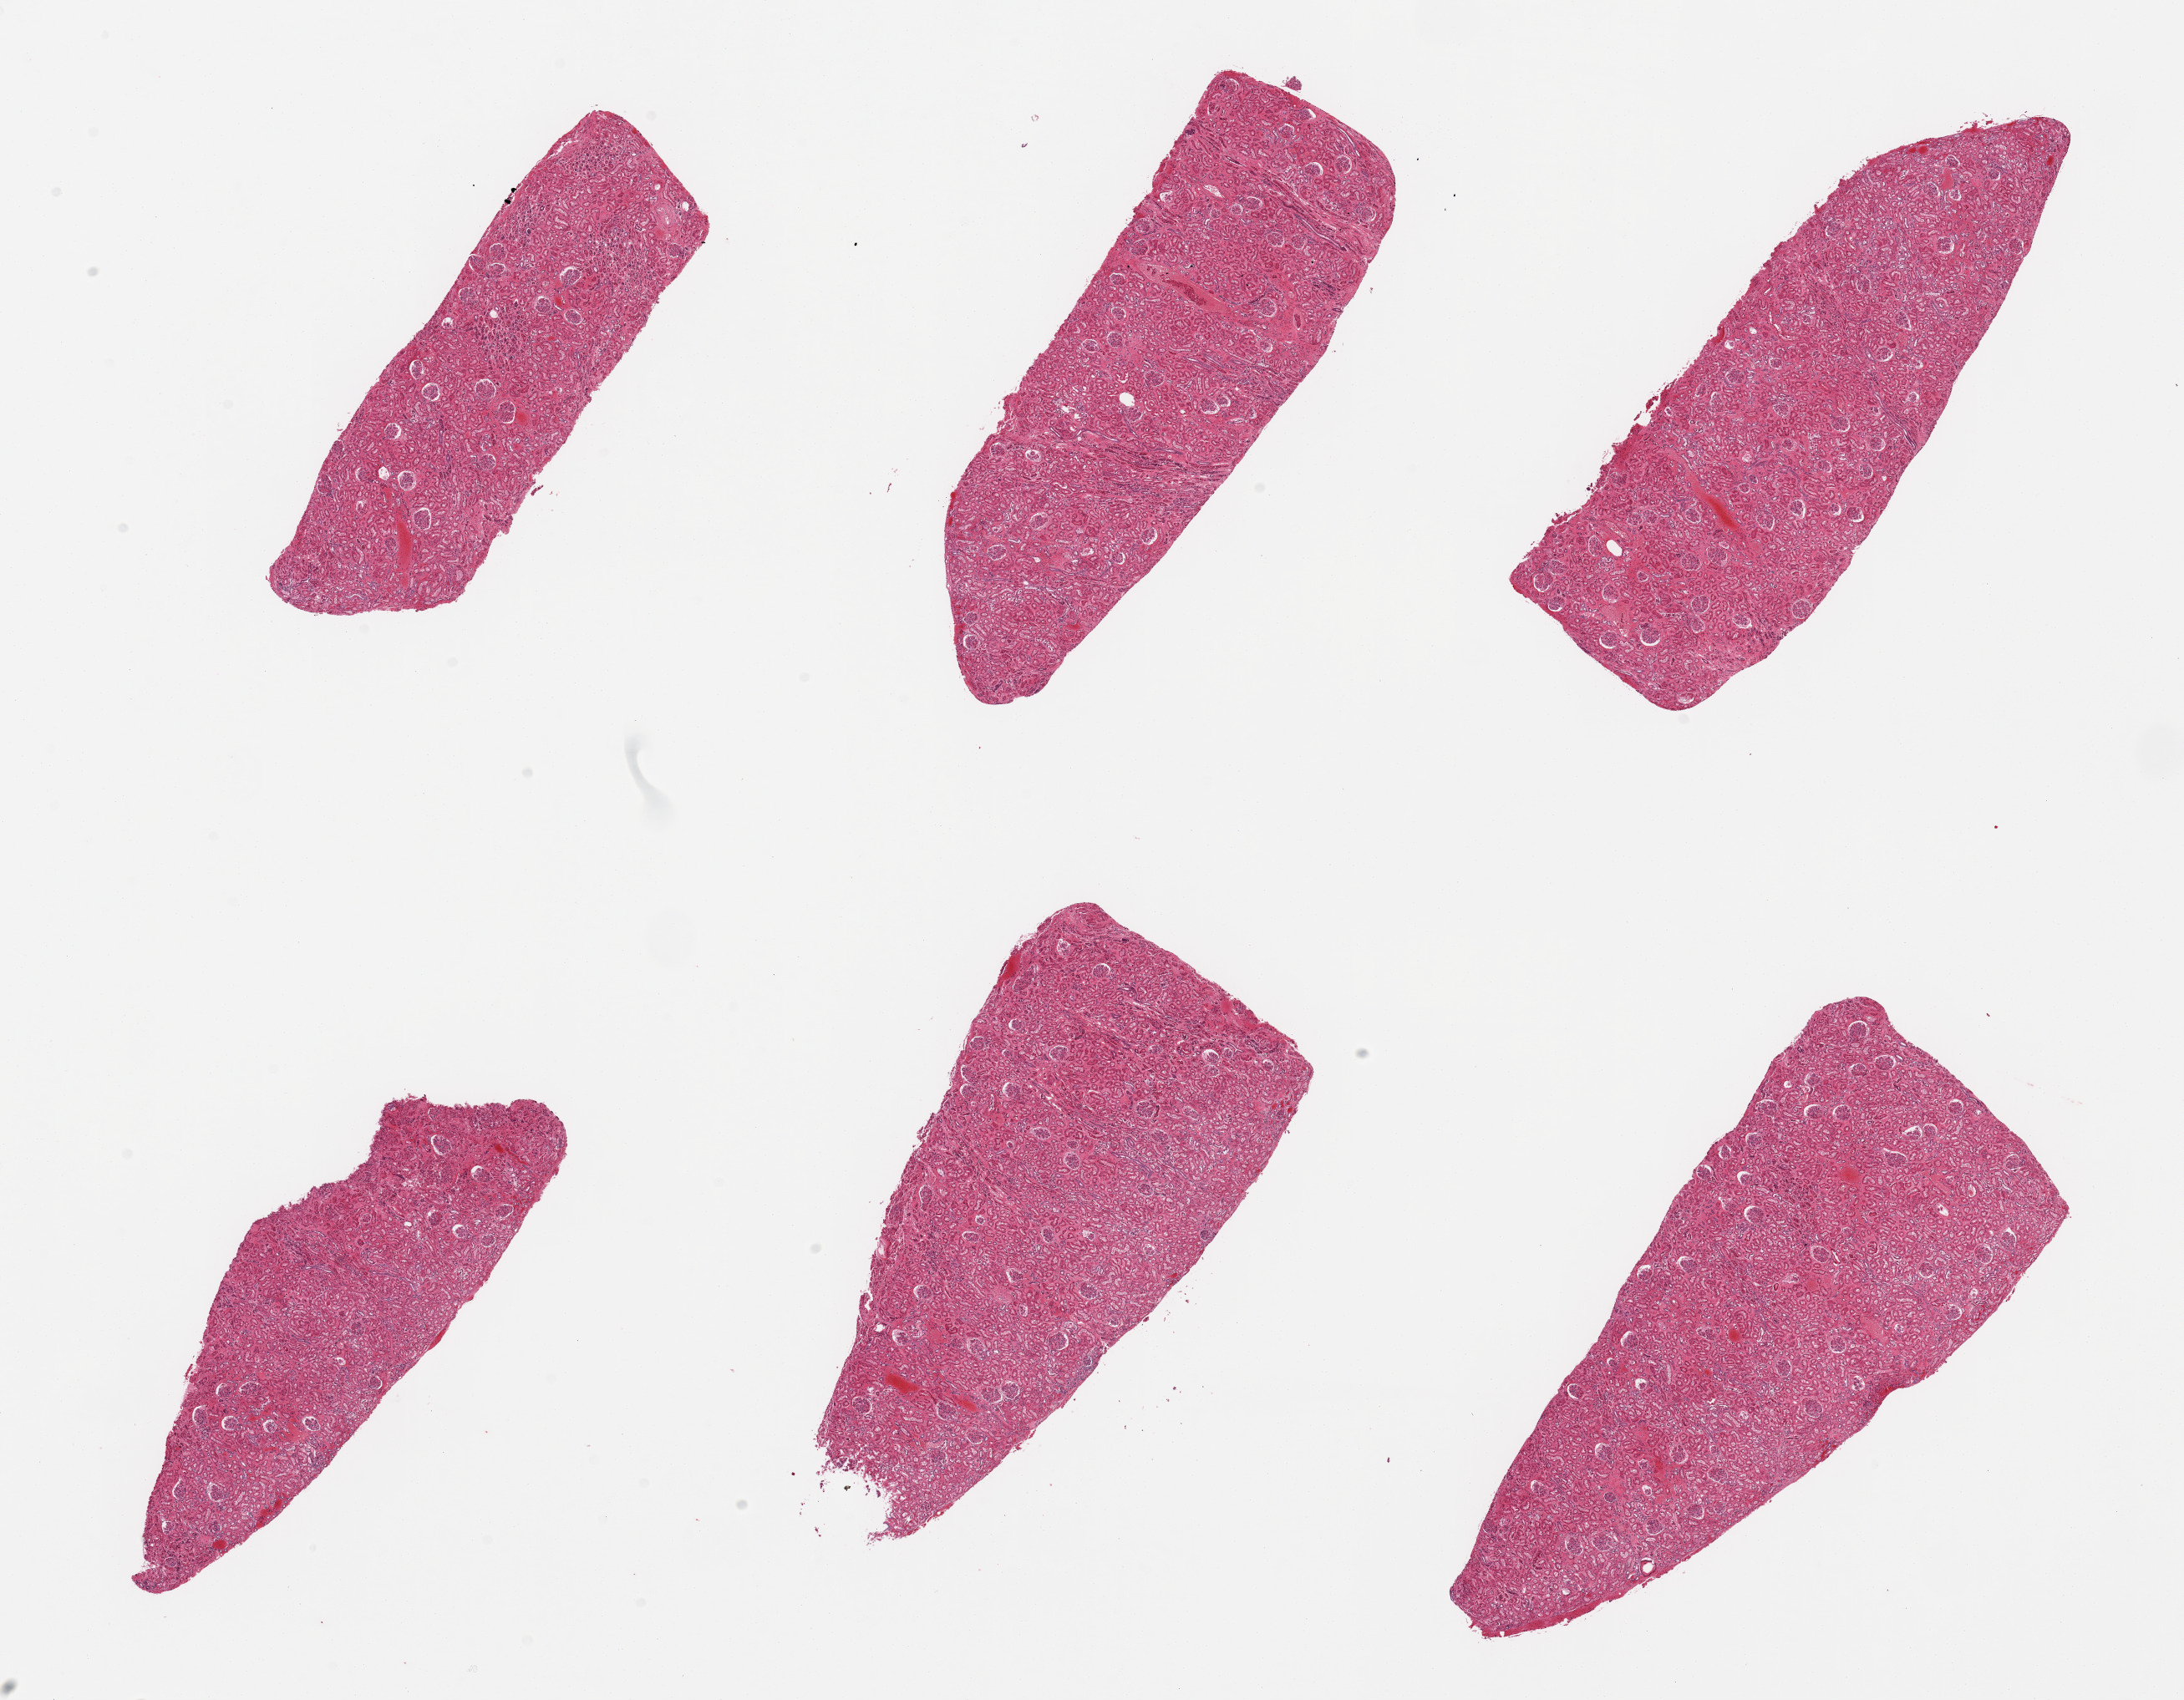
Digitized H&E-stained section — whole scanned area (about 20.7 x 16.1 mm) shown as a low-resolution overview; PAXgene-fixed, paraffin-embedded tissue; target tissue: renal cortex; donor tissue sample. Donor sex: female.
* reviewer comment on this tissue sample: 6 pieces; no lesions